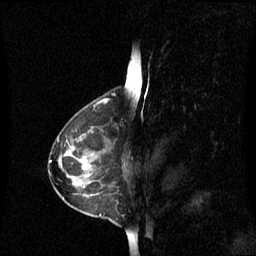
Breast MRI (dynamic contrast-enhanced), one sagittal slice; position 38 of 60 along the scan axis; dynamic contrast-enhanced series, image 2 of 3 at this slice position (ordered by acquisition); 1.5 T; TE 4.2 ms, TR 8.4 ms; 256 × 256 image matrix, field of view 240 × 240 mm. Patient: female, 42 years. From the clinical record (not read from this slice): setting: breast cancer imaged before/during neoadjuvant chemotherapy; receptor status: HR-positive, HER2-negative.
Annotated regions visible in this slice (semi-automatically segmented with operator editing):
- analysis volume of interest (the breast-tissue region the enhancement analysis was run in; not a lesion): box from (x=60, y=128) to (x=108, y=195) px
- tumour enhancement mask (voxels above the 70 % enhancement threshold inside the analysis volume of interest): (x=80, y=160)–(x=89, y=169)